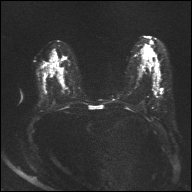
Breast MRI, one axial slice; position 18 of 32 along the scan axis; diffusion-weighted series; image 2 of 4 stored at this slice position (different b-values; order by instance number); 1.5 T; 4 mm slice thickness; 192 × 192 image matrix, field of view 360 × 360 mm. Female patient.
Annotated regions visible in this slice (manually delineated by an expert):
- tumour on diffusion-weighted imaging: bounding box (x1, y1, x2, y2) in pixels: (156, 86, 163, 91)